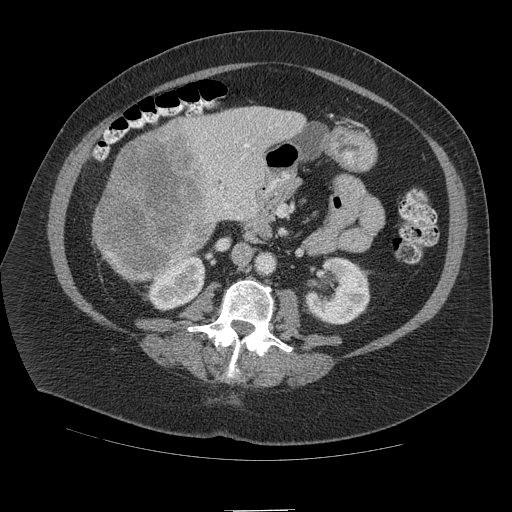
Contrast-enhanced abdominal CT (liver protocol), one axial slice. Position 38 of 109 along the scan axis. Reconstruction kernel STANDARD. Soft-tissue window (W 400 / L 40 HU). 2.5 mm slice thickness. 512 × 512 image matrix, field of view 420 × 420 mm. From the clinical record (not read from this slice): diagnosis: hepatocellular carcinoma (patient treated with transarterial chemoembolisation; whether this scan precedes or follows treatment is not stated here); TNM stage (as recorded): Stage-IVB; Child-Pugh class: A; tumour differentiation: poorly differentiated.
Structures marked on this image (semi-automatically segmented with operator editing):
- liver parenchyma outside the tumour (the mass and vessels are separate outlines, so this box may not span the whole liver): bounding box <92,106,306,280> (left, top, right, bottom; pixels)
- mass: <92,123,213,280>
- liver vessels: <209,124,278,210>